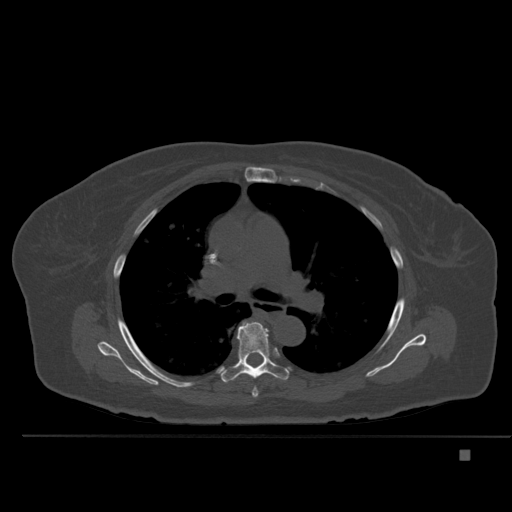
CT including the spine, one axial slice; position 342 of 477 along the scan axis; bone window (W 1800 / L 400 HU); 1.5 mm slice thickness; 512 × 512 image matrix. Patient: female, 74 years. From the clinical record (not read from this slice): primary cancer: colon.
Outlined on this slice (semi-automatically segmented with operator editing):
- T5 vertebra: box from (x=252, y=371) to (x=258, y=399) px
- T6 vertebra: (x=219, y=322)–(x=289, y=383)